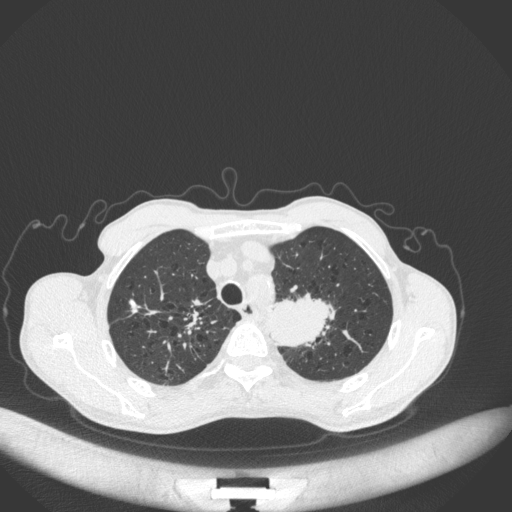
Chest CT, one axial slice; slice 344 of 394 in the series (ordered by position); reconstruction kernel B31f; lung window (W 1500 / L -600 HU); 1 mm slice thickness; 512 × 512 image matrix. Male patient, age 65 years. From the clinical record (not read from this slice): clinical TNM (as recorded): T2b N0 M0; histopathological grade: G2.
Outlined on this slice (bounding box drawn by a radiologist):
- lung tumour (recorded histology: adenocarcinoma): box from (x=262, y=287) to (x=334, y=347) px